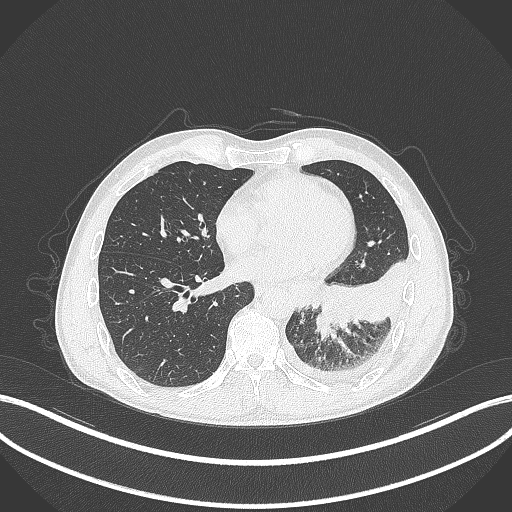
Chest CT, one axial slice. Position 115 of 295 along the scan axis. Reconstruction kernel B70f. Lung window (W 1500 / L -600 HU). 1 mm slice thickness. 512 × 512 image matrix, field of view 400 × 400 mm. Patient: male, 47 years. From the clinical record (not read from this slice): clinical TNM (as recorded): T3 N1 M1c; histopathological grade: G3.
Structures marked on this image (rectangle marked by the reading radiologist):
- lung tumour (recorded histology: small cell carcinoma): bounding box <311,308,331,340> (left, top, right, bottom; pixels)